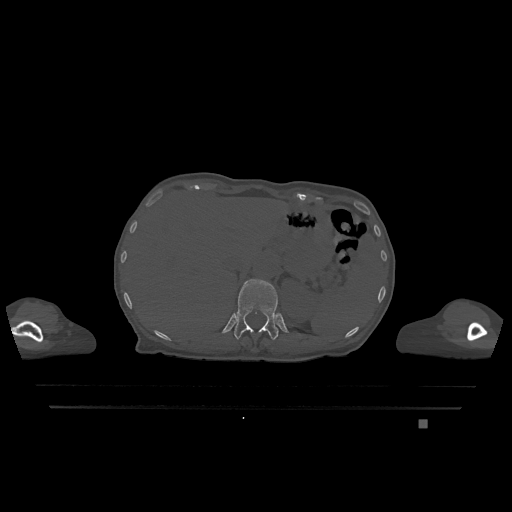
CT including the spine, one axial slice; position 540 of 1317 along the scan axis; bone window (W 1800 / L 400 HU); 0.5 mm slice thickness; 512 × 512 image matrix. Patient: female, 74 years. Case-level facts recorded for this patient, not image findings: primary cancer: lung.
Outlined on this slice (semi-automatic segmentation, software-assisted and operator-edited):
- T12 vertebra: bounding box [x1, y1, x2, y2] px = [234, 279, 279, 340]